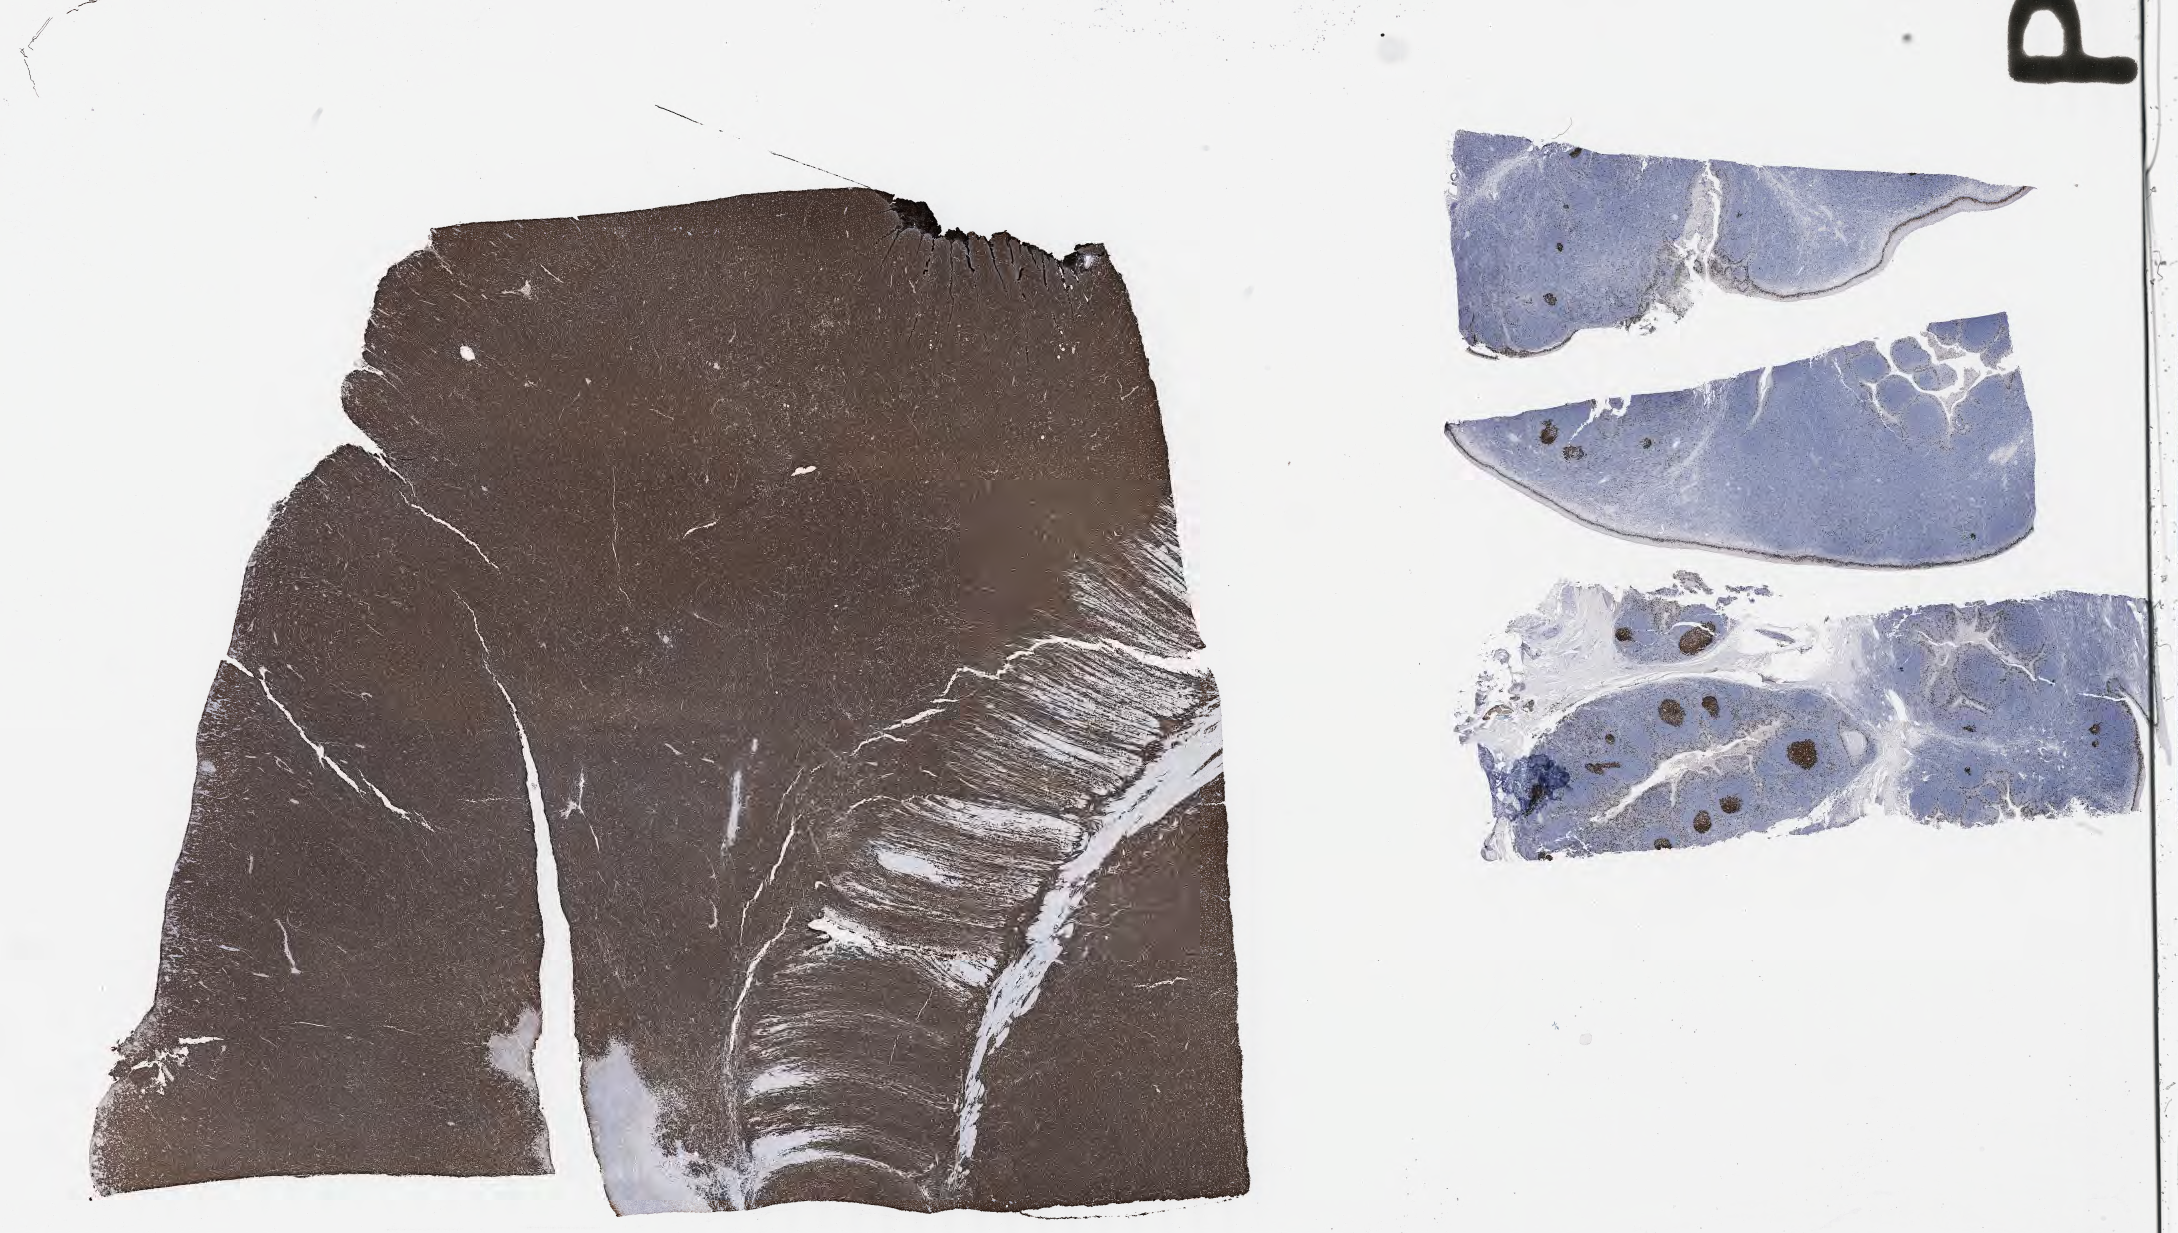
Immunohistochemistry (IHC) whole-slide image stained for Ki-67, whole scanned area (about 35.2 x 19.9 mm) shown as a low-resolution overview. Specimen: tumor tissue. Site: colon. Male patient, aged 14.
Histologic diagnosis: Burkitt lymphoma, NOS.